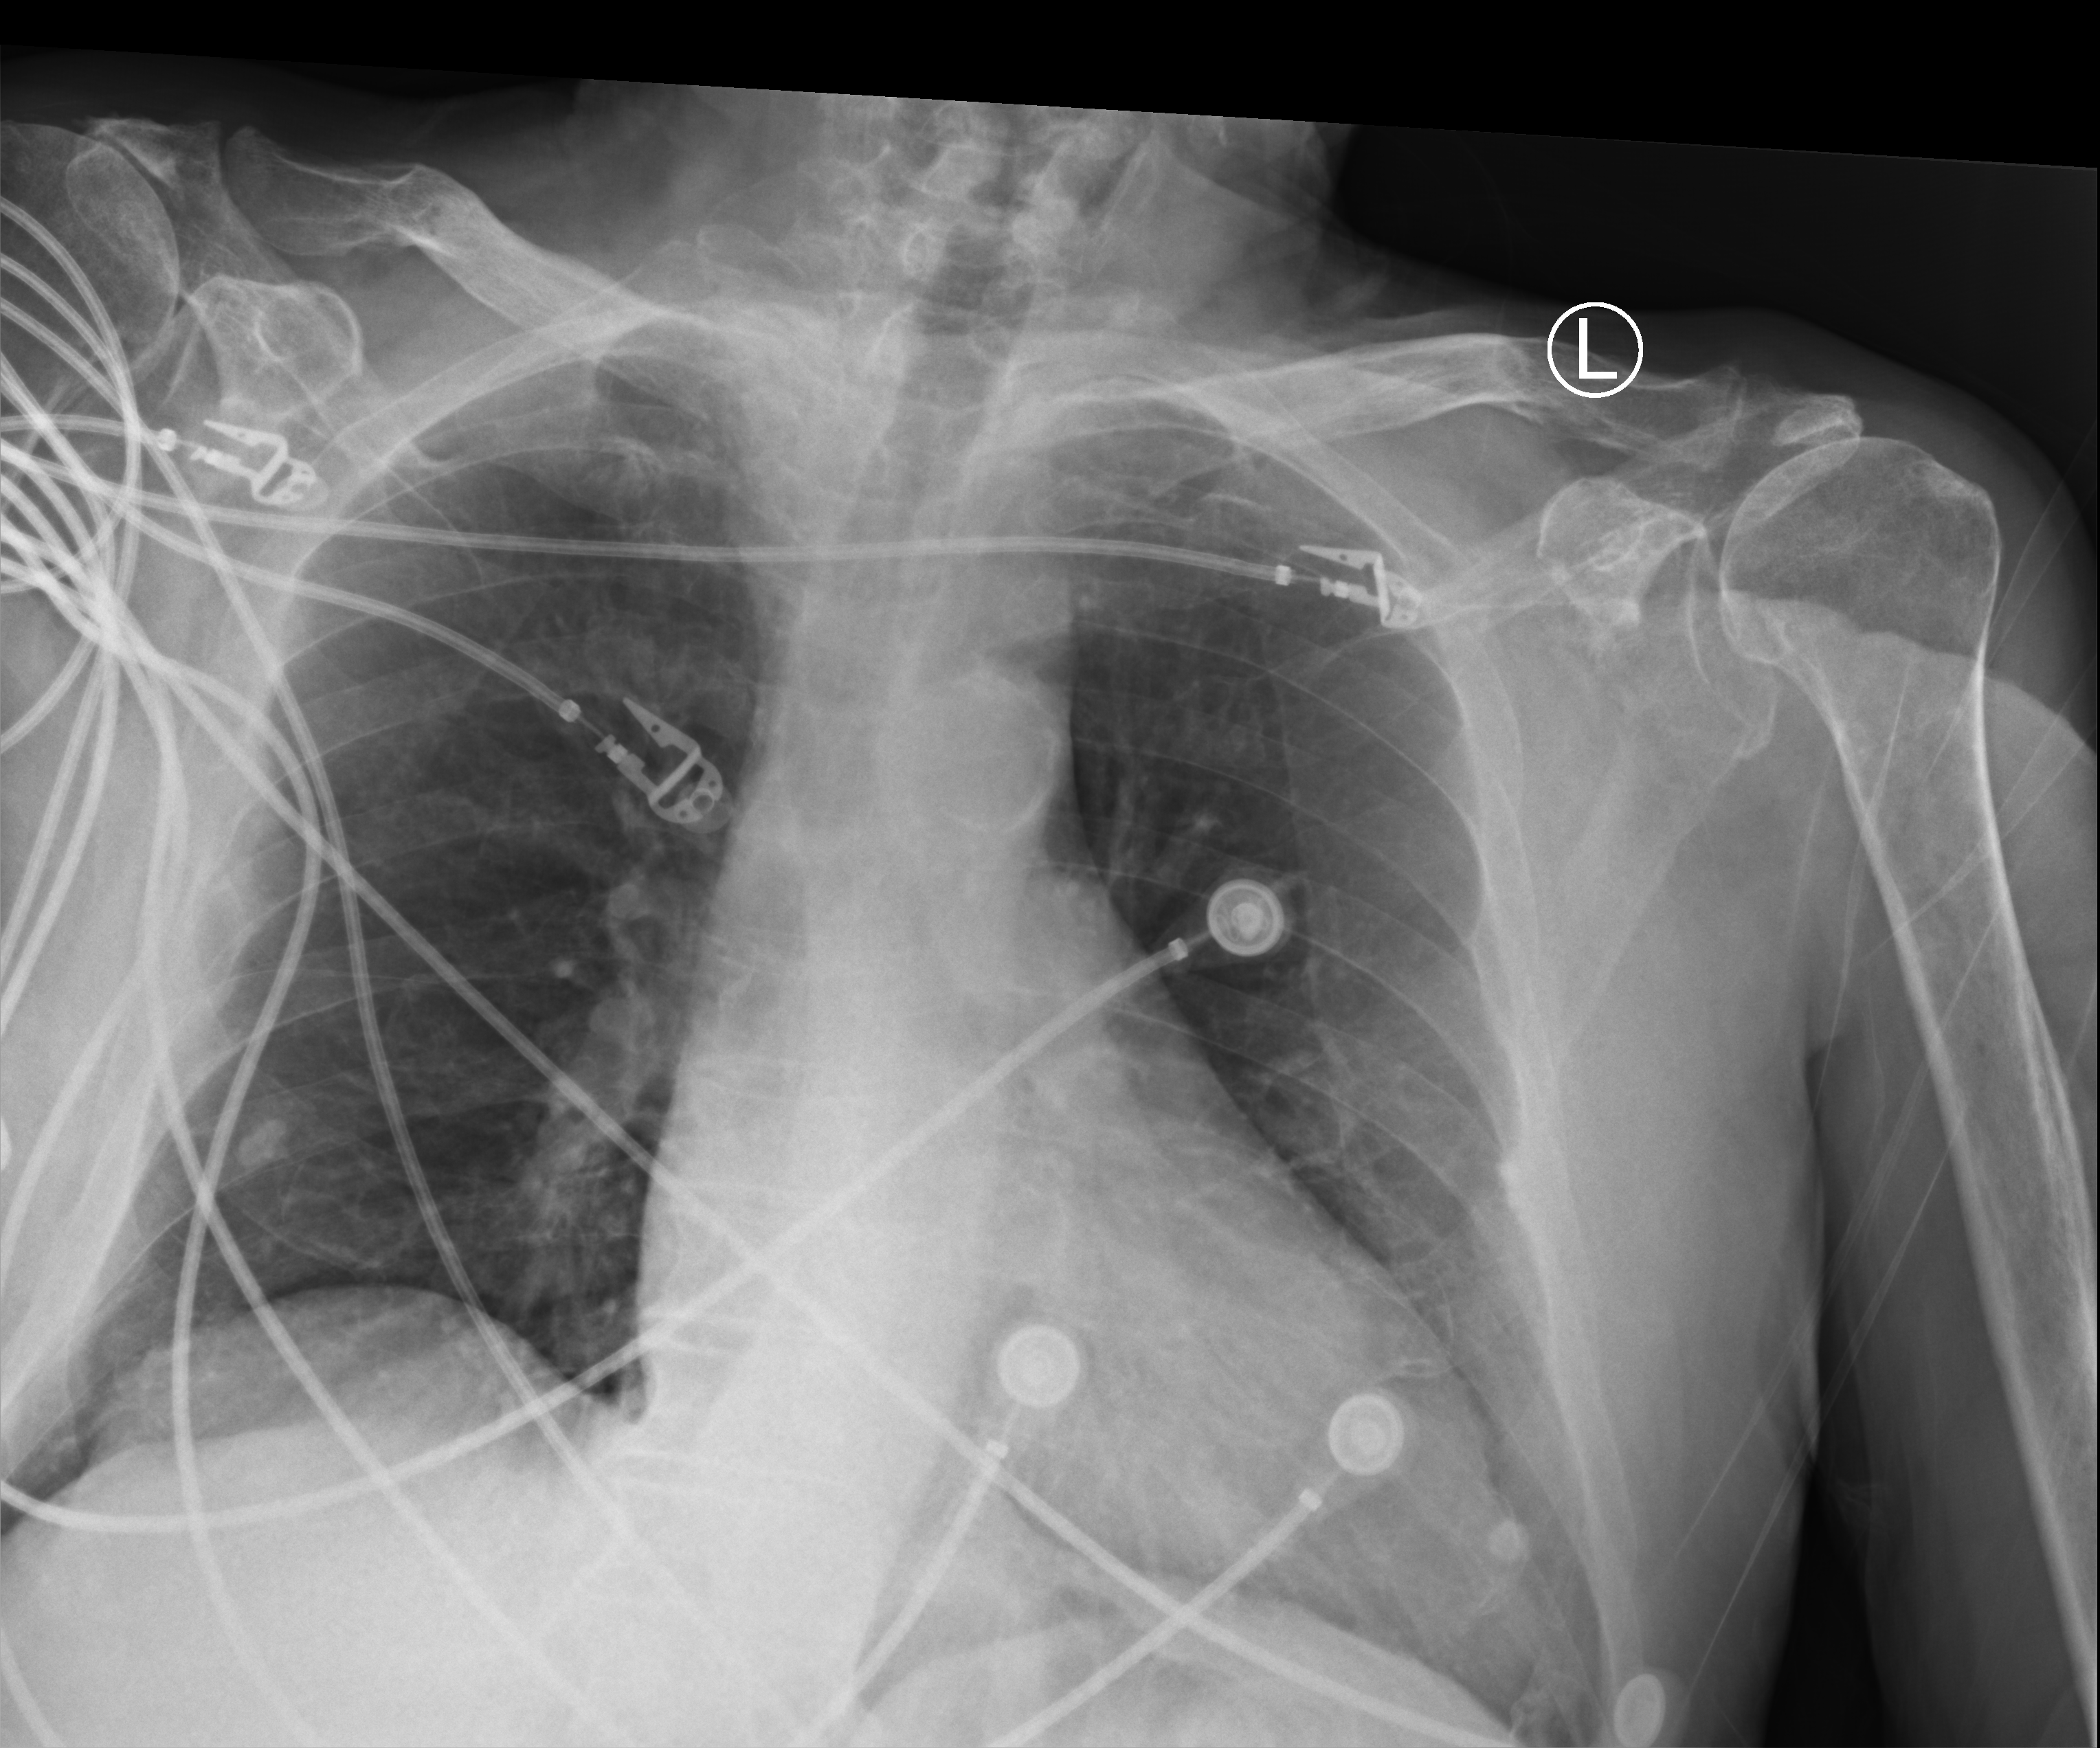
Chest X-ray (portable), anteroposterior (AP) projection. Male patient hospitalised with COVID-19, age 75–90 years.
From the hospital-stay record, not from the radiograph (when in the stay this image was taken is not recorded): admitted to intensive care during this hospital stay: no.